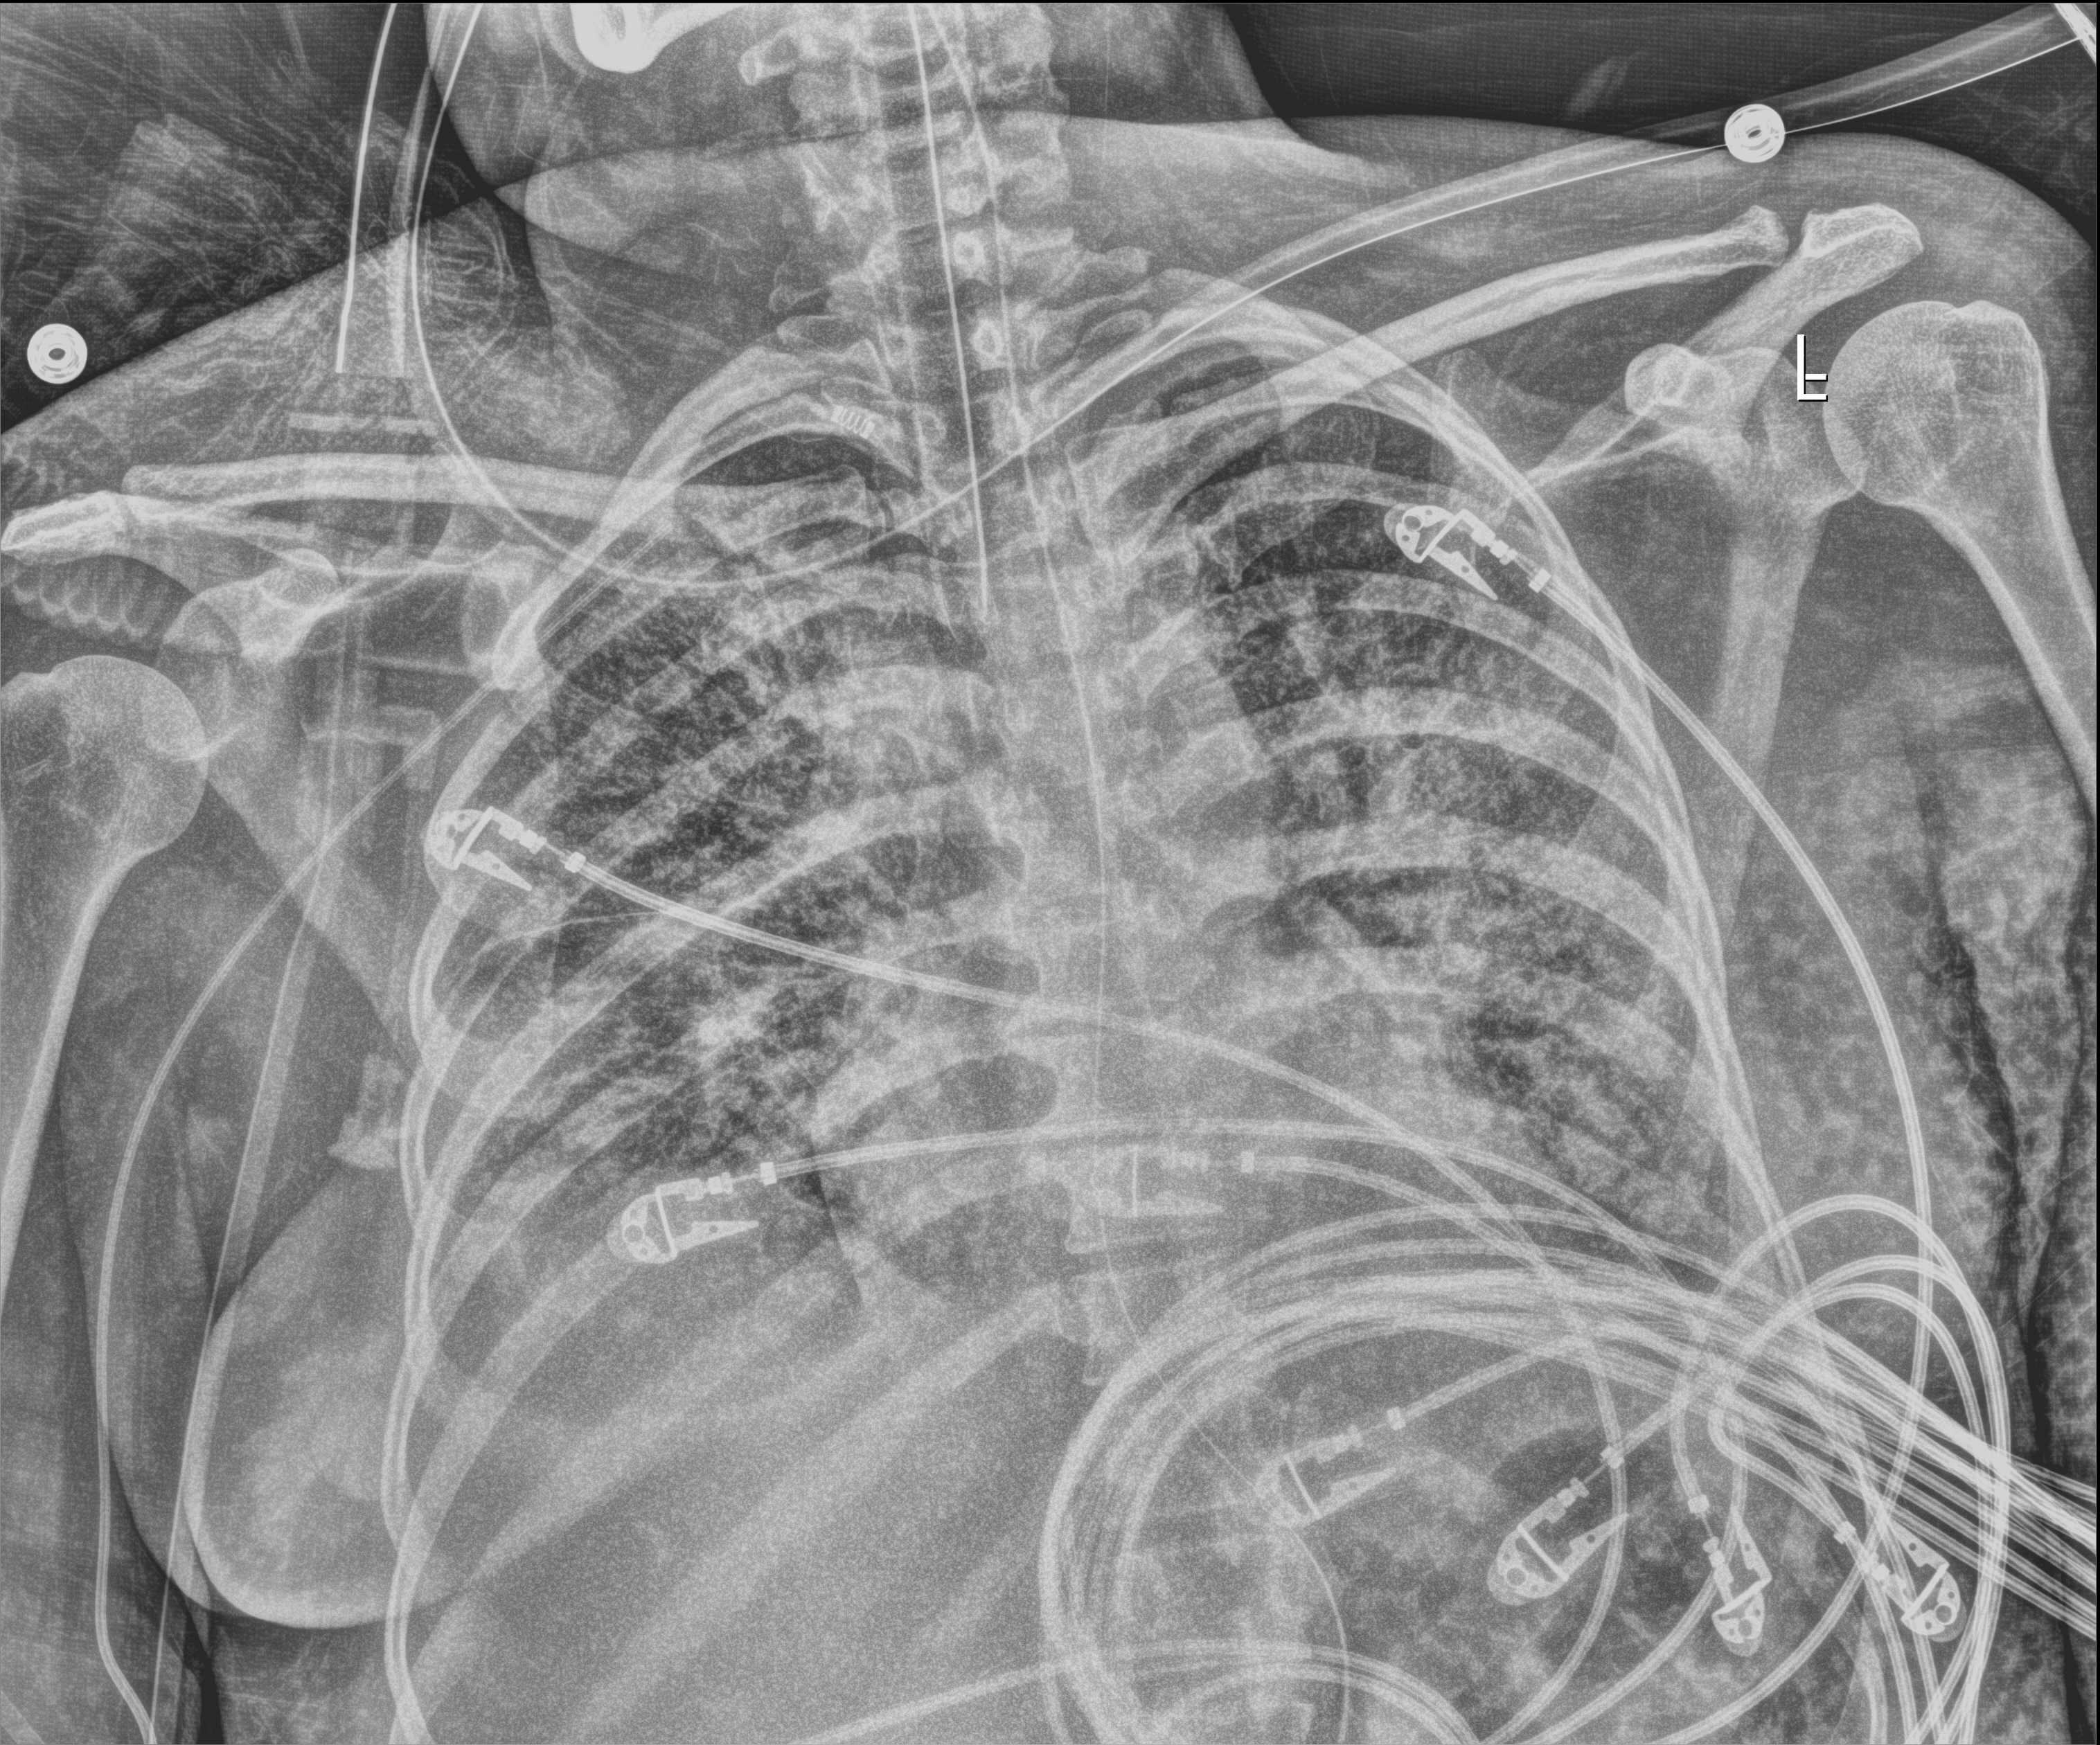
Chest radiograph, anteroposterior (AP) projection. Female patient hospitalised with COVID-19, age 18–59 years.
From the hospital-stay record, not from the radiograph (when in the stay this image was taken is not recorded):
- other chronic lung disease (admission record): no
- mechanically ventilated during this hospital stay: yes
- admitted to intensive care during this hospital stay: yes